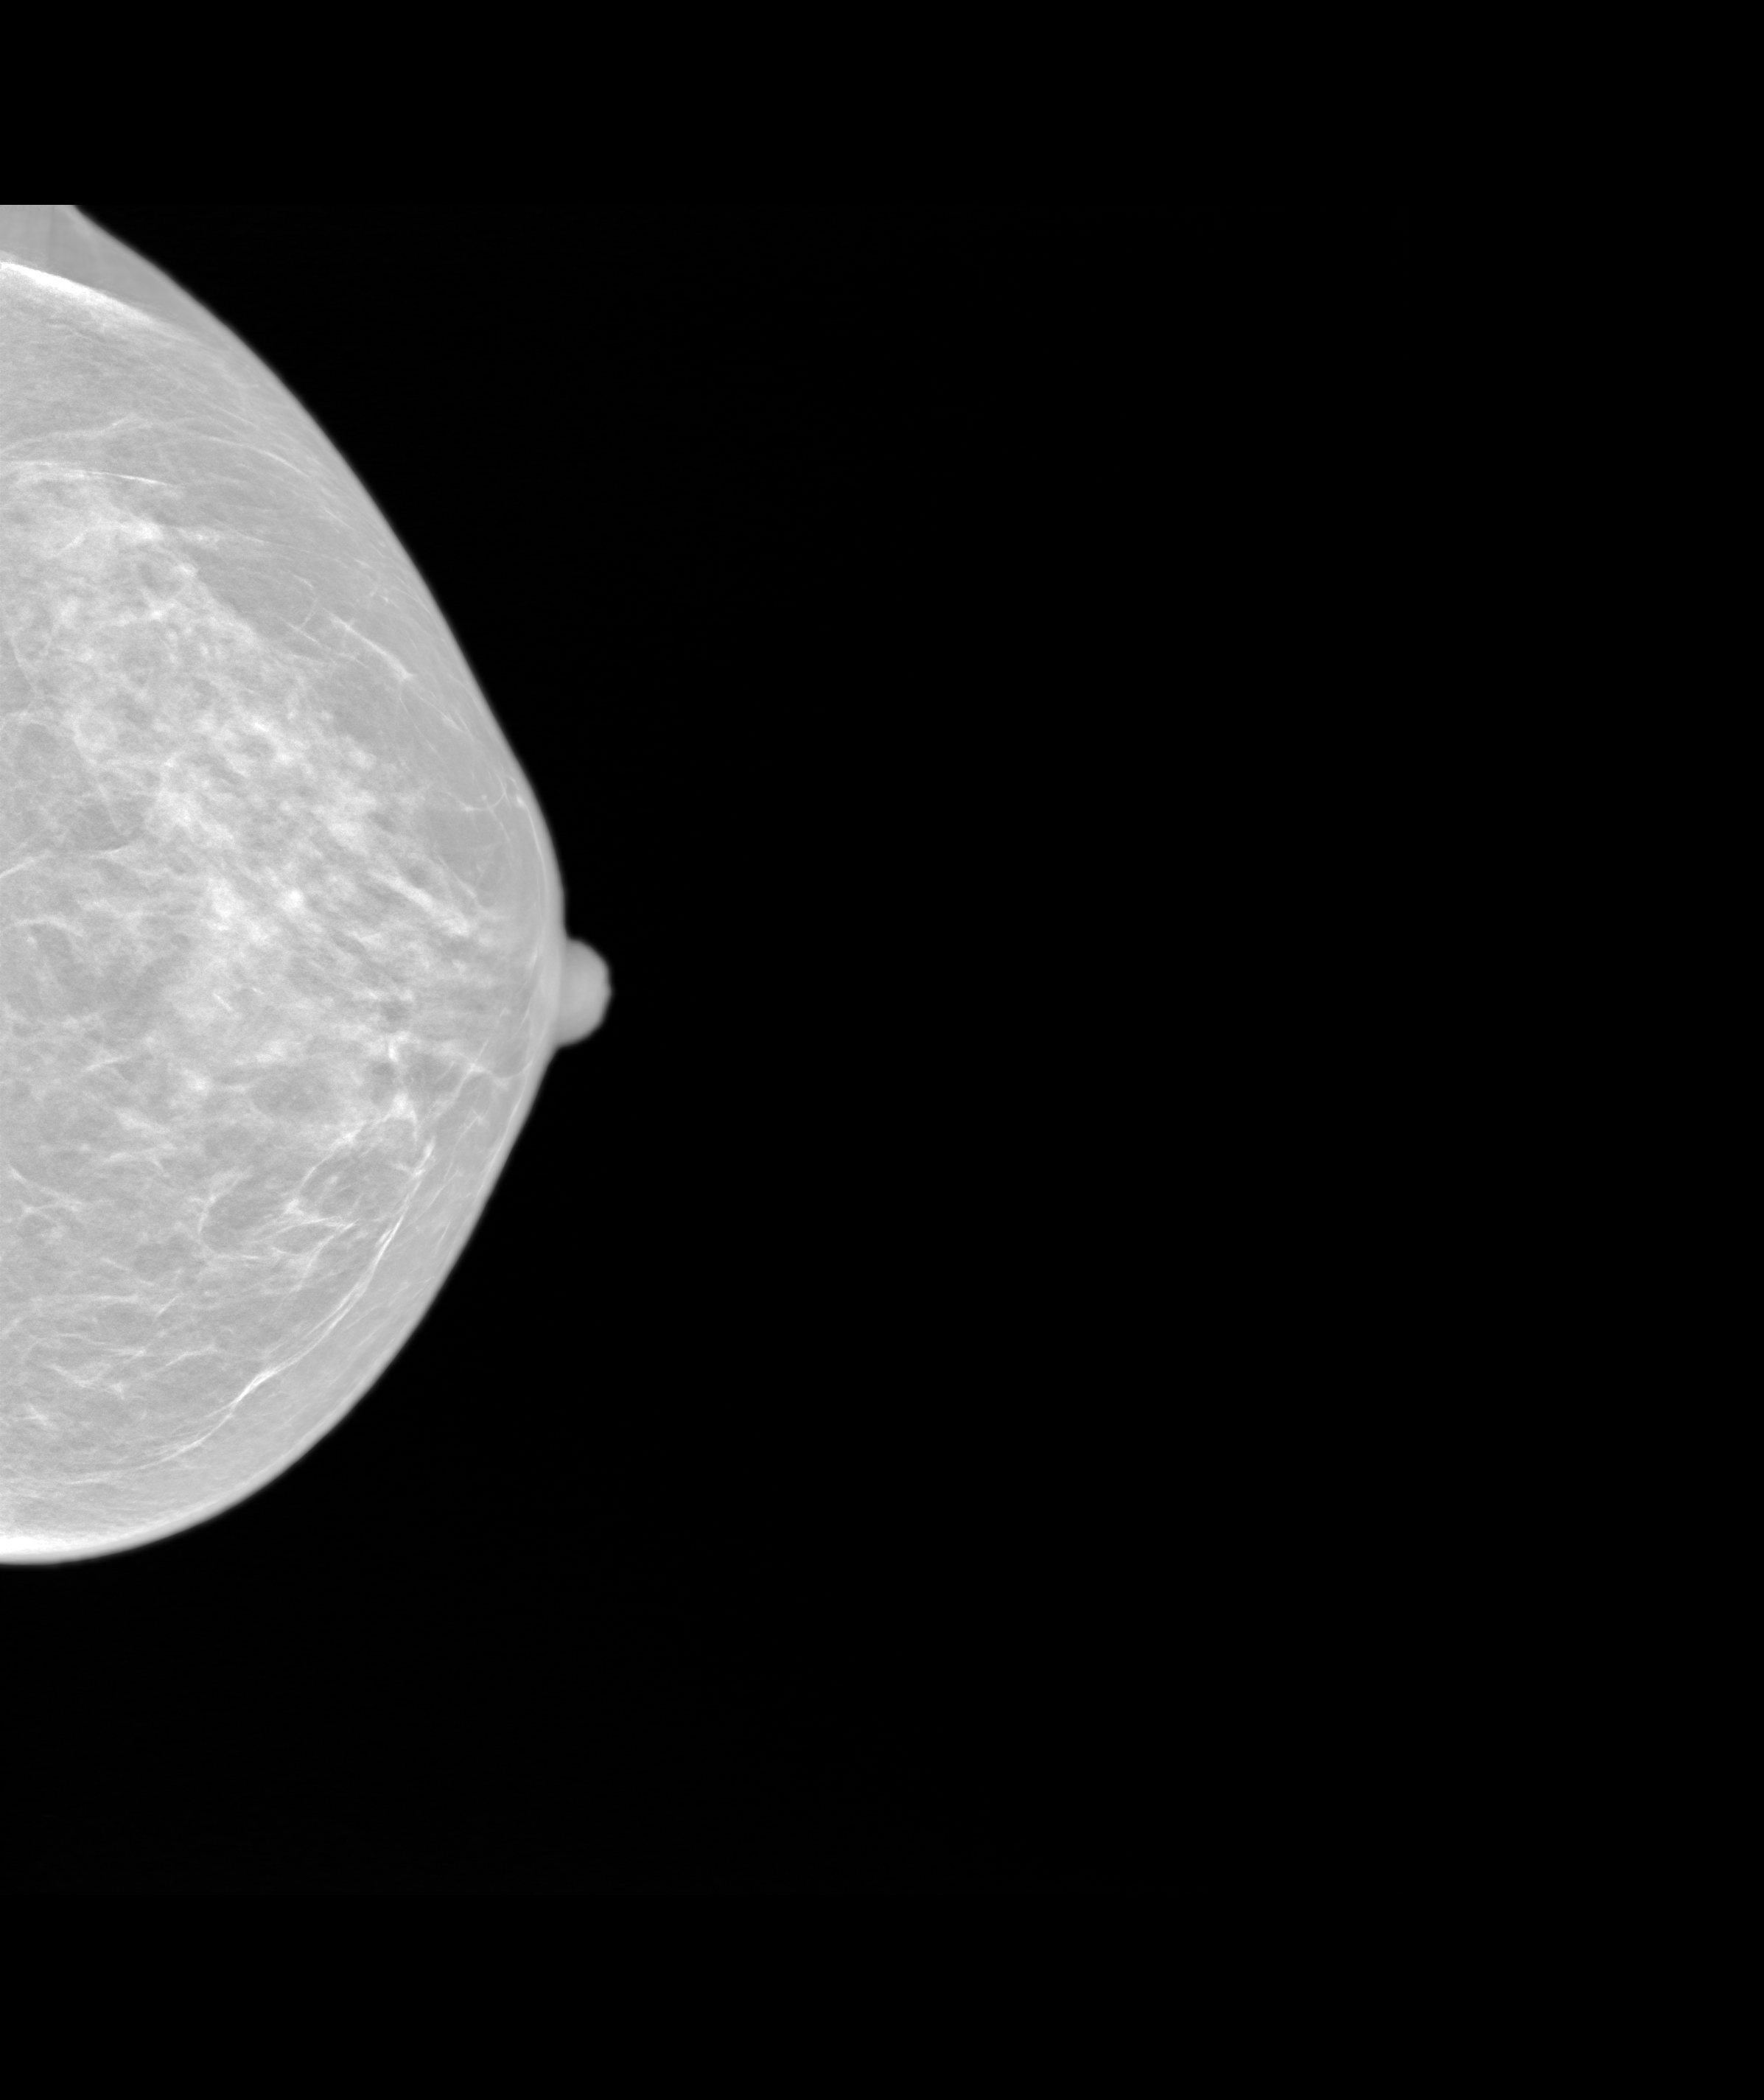
Screening examination; system: SenoIris_1SP2(440). Female patient, age 62 years.
Image type: synthesized 2-D view from tomosynthesis. Breast: left. Projection: cranio-caudal projection.